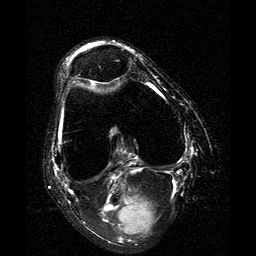
MRI of an extremity soft-tissue mass, one axial slice. Position 7 of 25 along the scan axis. T2-weighted fat-saturated. 256 × 256 image matrix. Female patient. Case-level facts recorded for this patient, not image findings: histological type: liposarcoma; site of the primary tumour: right thigh.
Annotated regions visible in this slice (manually delineated by an expert):
- gross tumour volume (mass): box from (x=98, y=193) to (x=158, y=239) px